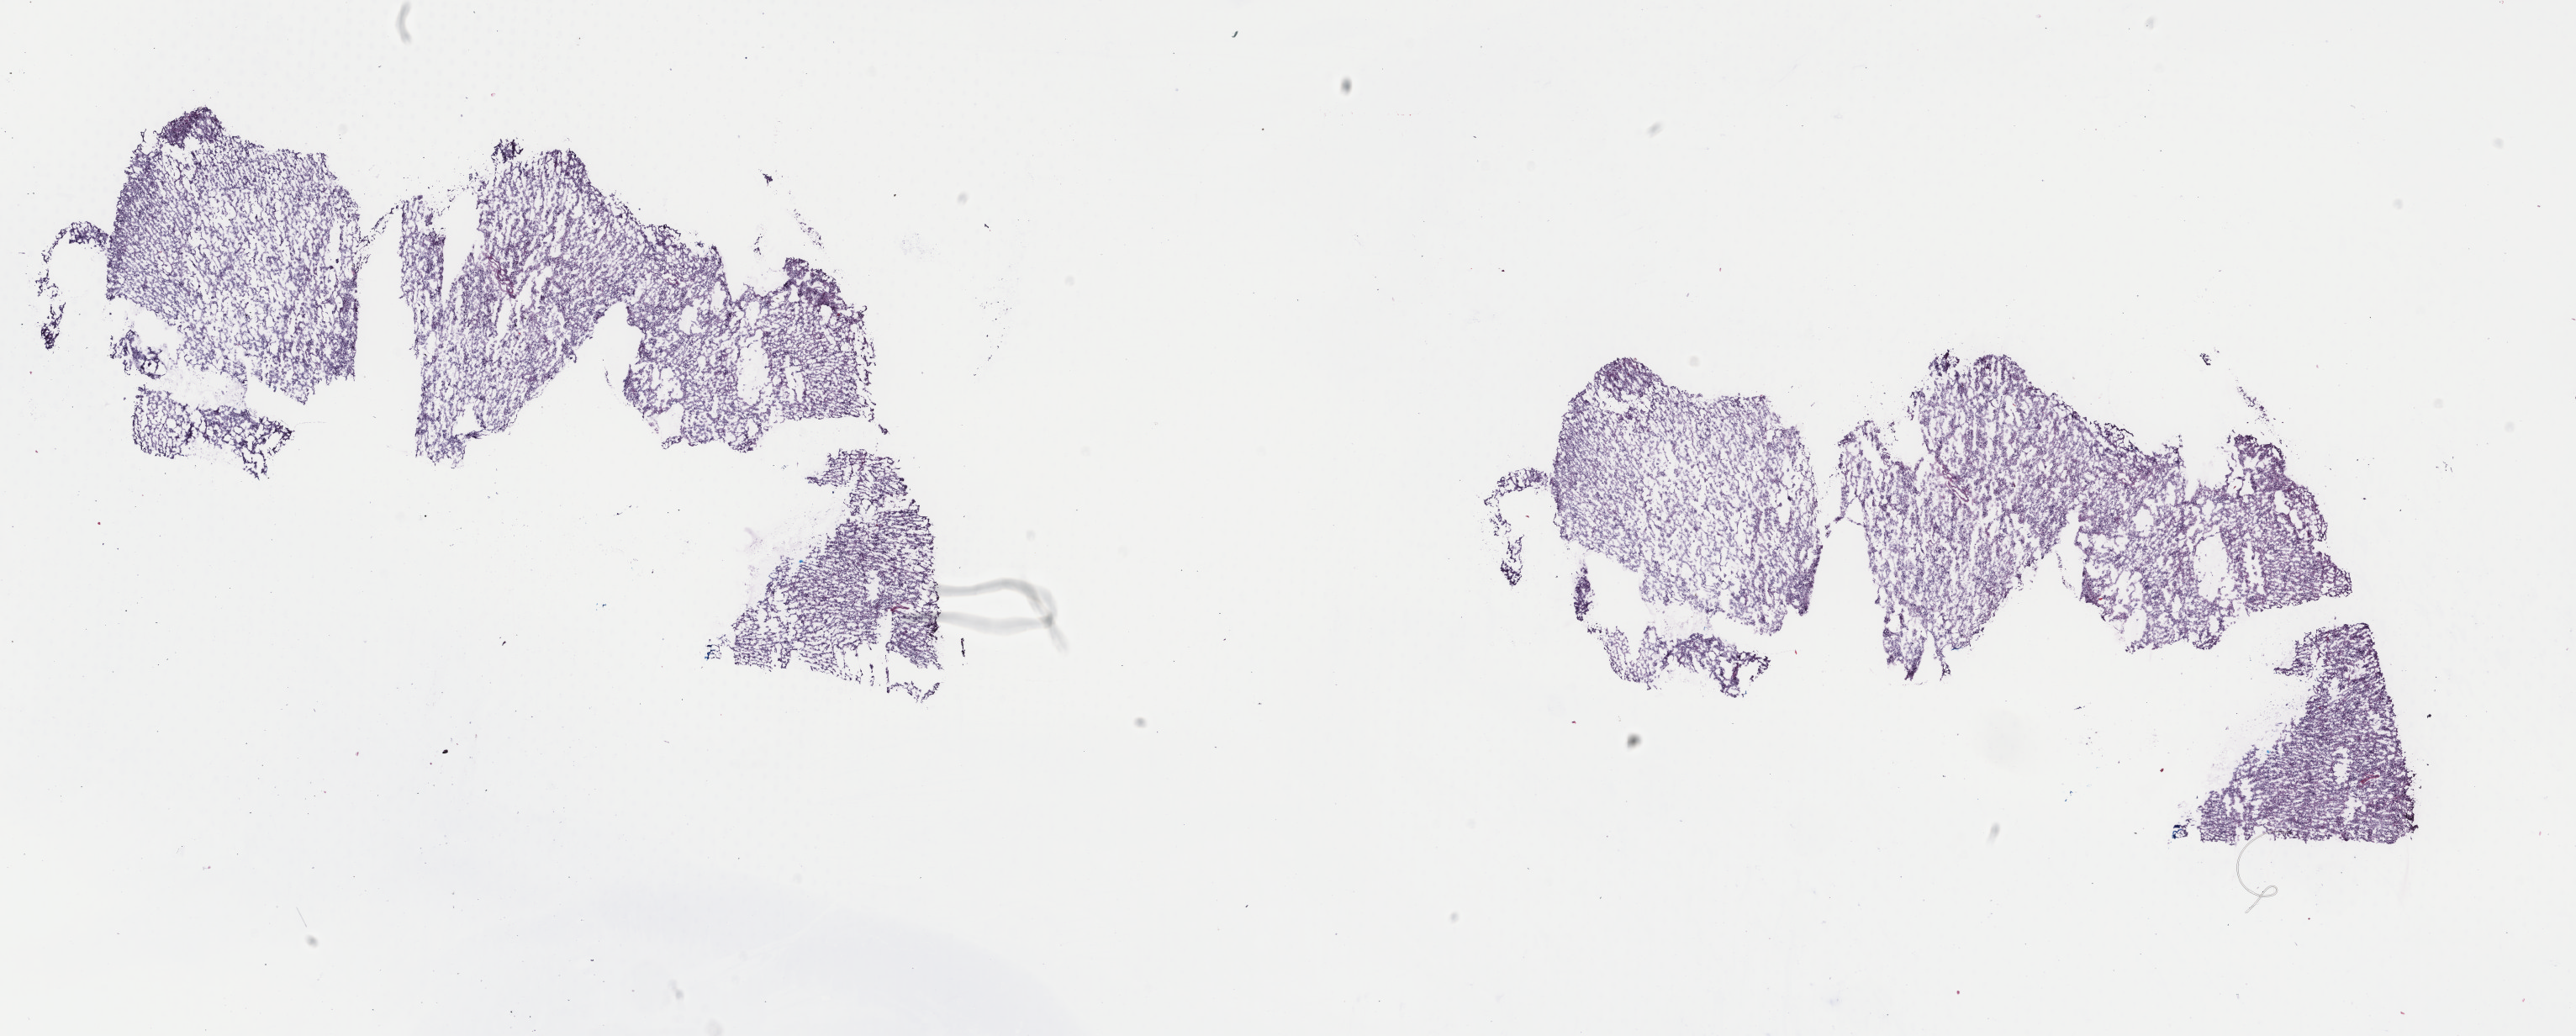
Digitized Hematoxylin and eosin (H&E) stained tissue section (whole slide), shown as a low-resolution overview of the whole scanned area (about 24.3 x 9.8 mm, from a 40x scan). Frozen section from the top of the tissue portion. Primary tumour sample from the brain. Female patient; age at initial diagnosis 27 years.
Pathologic diagnosis: Oligodendroglioma, NOS.